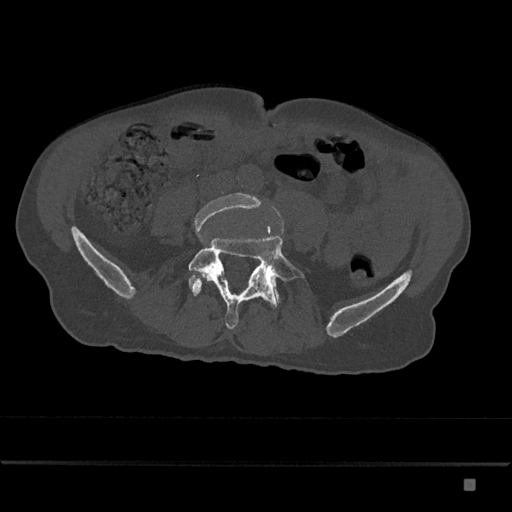
CT including the spine, one axial slice; slice 291 of 797 in the series (ordered by position); reconstruction kernel Br40s/3; bone window (W 1800 / L 400 HU); 0.5 mm slice thickness; 512 × 512 image matrix, field of view 390 × 390 mm. Patient: male, 72 years. From the clinical record (not read from this slice): primary cancer: prostate.
Outlined on this slice (semi-automatic segmentation, software-assisted and operator-edited):
- L4 vertebra: bounding box (x1, y1, x2, y2) in pixels: (193, 193, 262, 279)
- L5 vertebra: (188, 236, 304, 329)